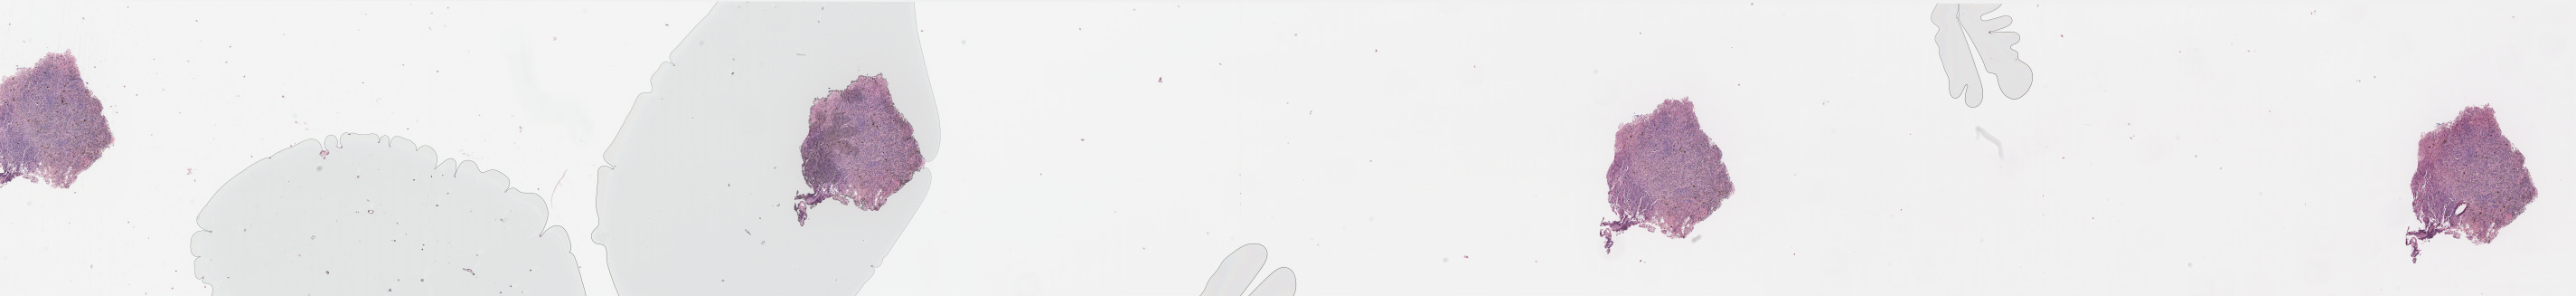
Digitized Hematoxylin and eosin (H&E) stained tissue section (whole slide) — a low-resolution overview of the entire scanned area, about 45.7 x 5.2 mm (slide scanned at 40x); FFPE section; sample: primary tumour, skin. Male, age 55 years at initial diagnosis.
• histologic diagnosis: Malignant melanoma, NOS